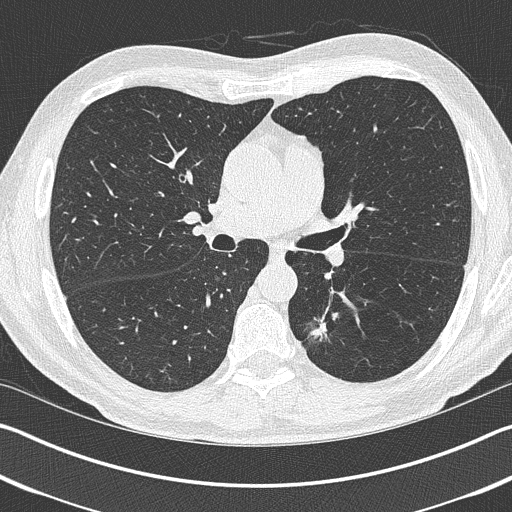
Low-dose screening chest CT, one axial slice; slice 241 of 402 in the series (ordered by position); 120 kVp; lung window (W 1500 / L -600 HU); 1 mm slice thickness; 512 × 512 image matrix, field of view 340 × 340 mm.
Annotated regions visible in this slice (expert manual segmentation):
- lesion 1 (tumor, lower lobe of left lung): bounding box [x1, y1, x2, y2] px = [310, 313, 339, 341]